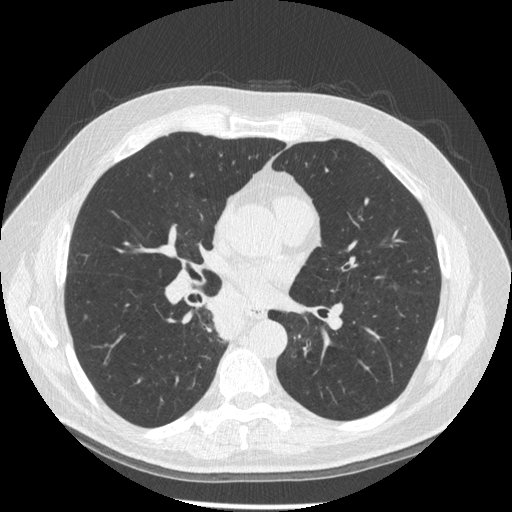
Low-dose screening chest CT, one axial slice; position 95 of 181 along the scan axis; reconstruction kernel STANDARD; lung window (W 1500 / L -600 HU); 1.25 mm slice thickness; 512 × 512 image matrix, field of view 370 × 370 mm.
Annotated regions visible in this slice (manually delineated by an expert):
- lesion 1 (tumor, lower lobe of right lung): bounding box (x1, y1, x2, y2) in pixels: (211, 299, 245, 339)